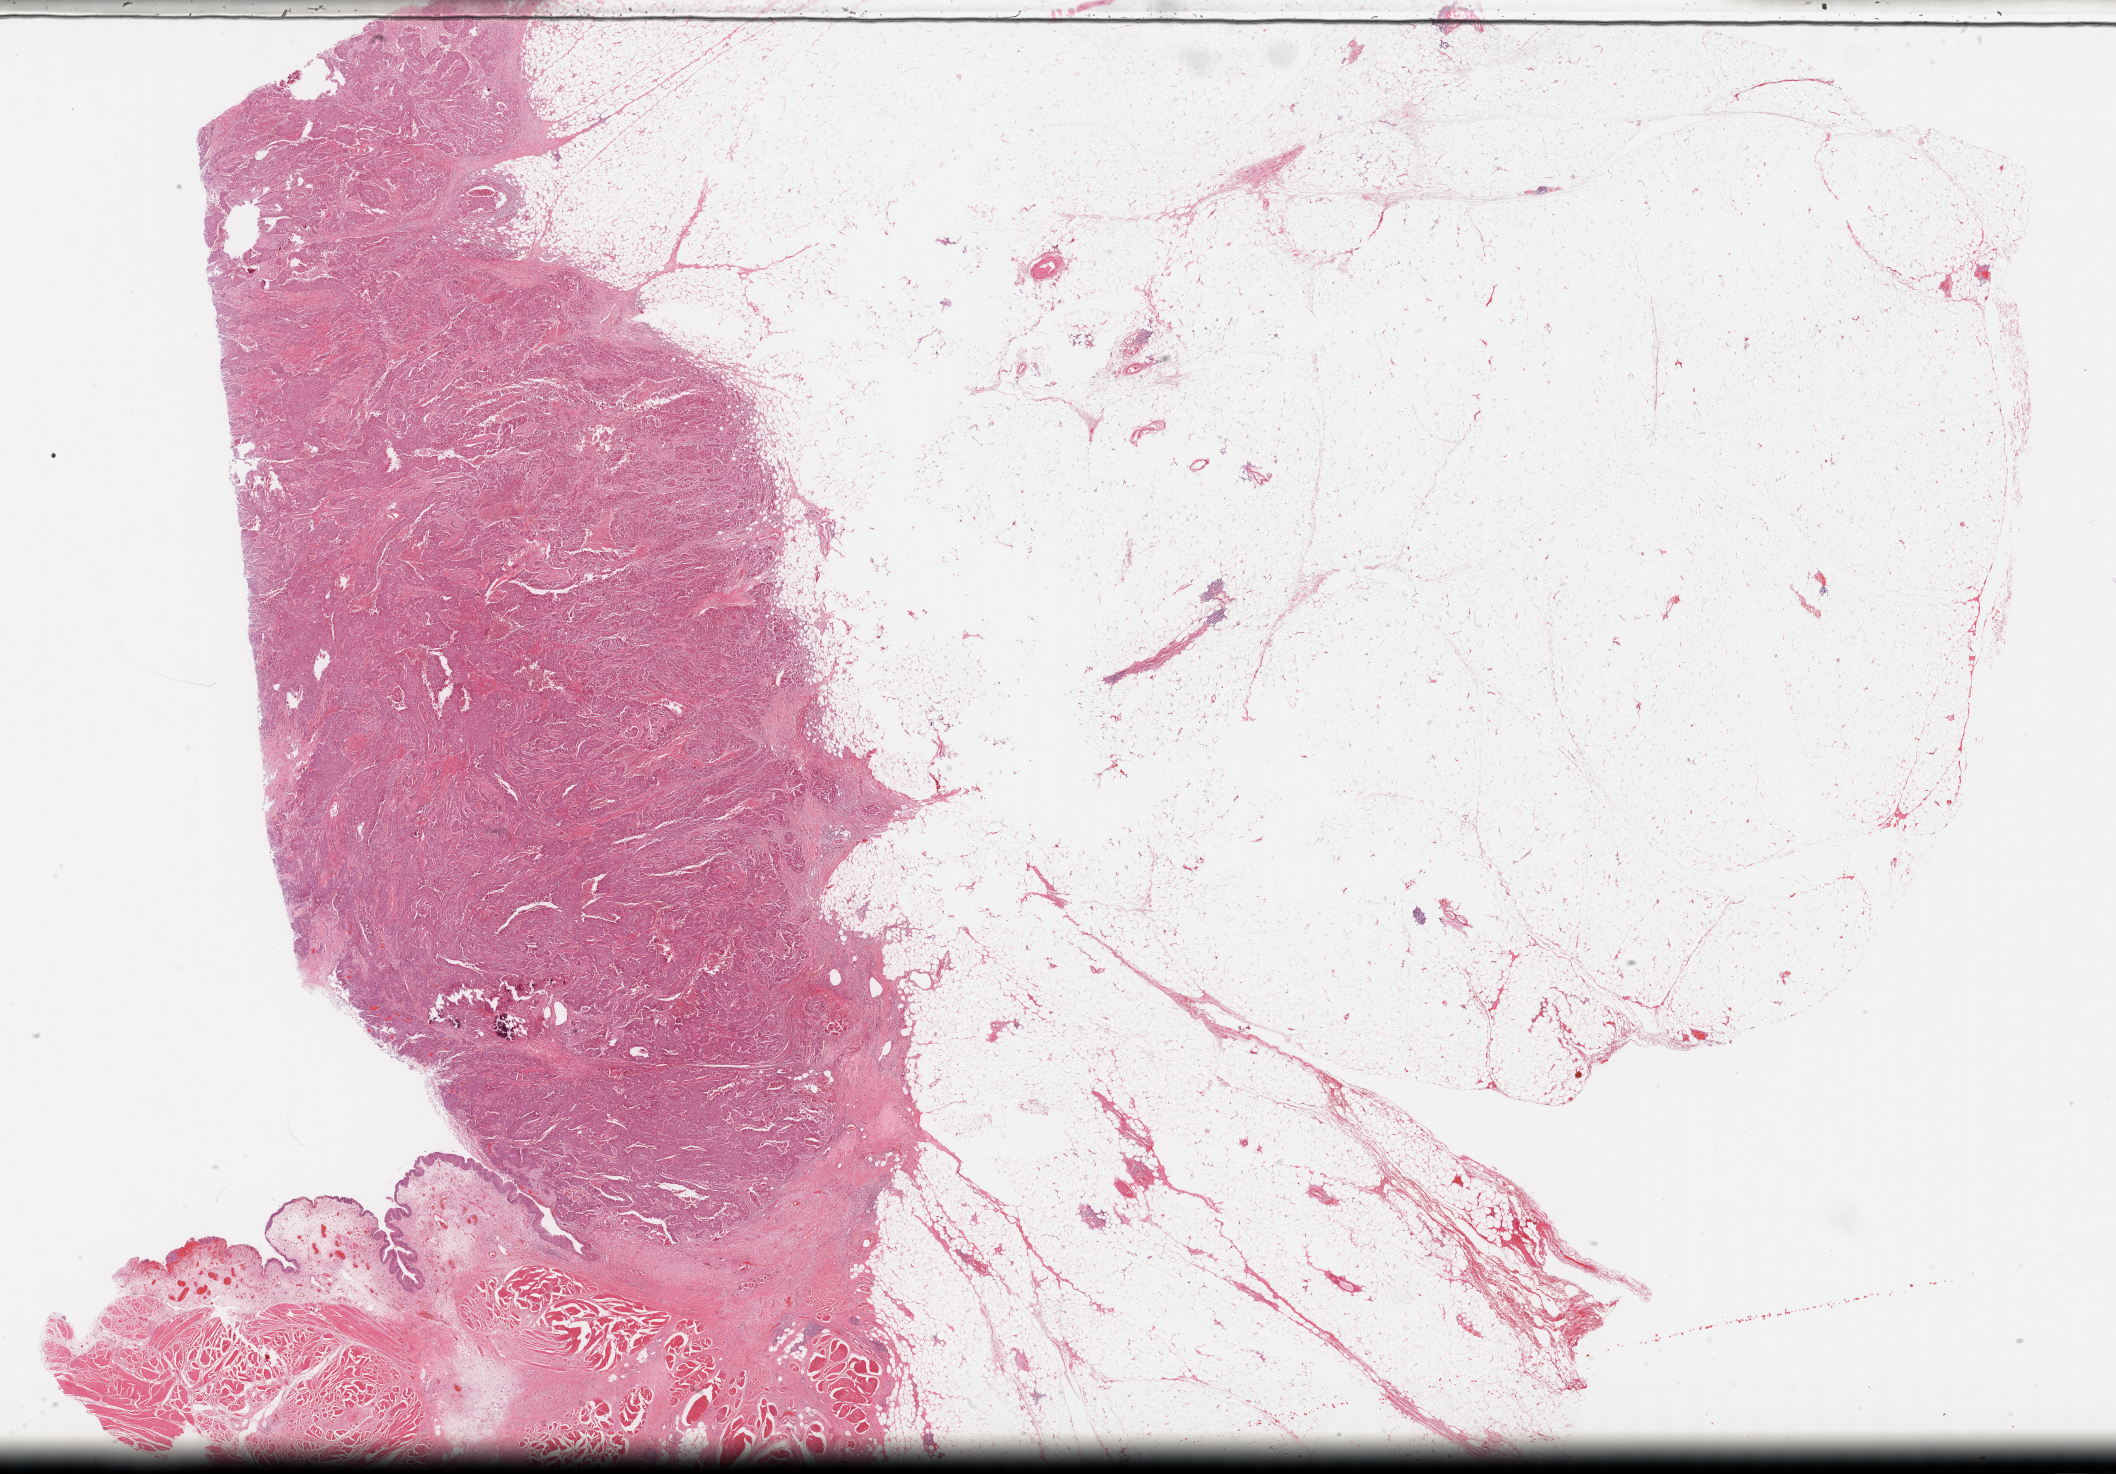
Hematoxylin and eosin (H&E) stained whole-slide image, a low-resolution overview of the entire scanned area, about 34.2 x 23.8 mm (acquisition: 40x scan). FFPE section. Bladder, primary tumour sample. Male, age 66 years at initial diagnosis. Histologic grade: high grade.
Lymph nodes positive (case pathology): 0 of 20 examined. AJCC pathologic stage: III (6th edition). Pathologic diagnosis: Transitional cell carcinoma.